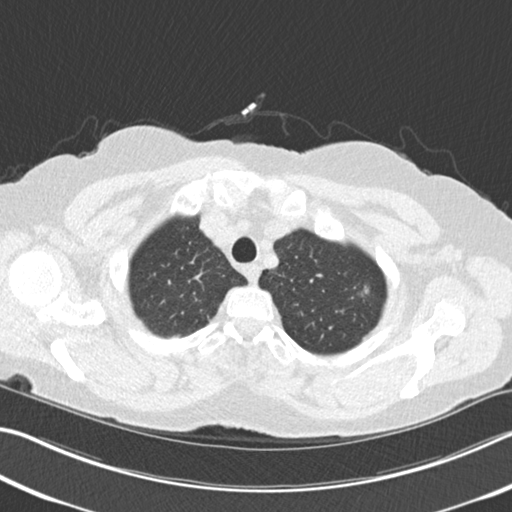
Chest CT (low-dose screening protocol), one axial image, second screening round (one year after baseline), lung window (W 1500 / L -600 HU), standard (soft-tissue) reconstruction kernel (B30f), slice 29 of 225 in the series, 512 × 512 image matrix. Female participant, aged 64 years at enrolment.
- Expert-annotated lung lesion, bounding box (x1, y1, x2, y2) in pixels: (343, 274, 377, 307).
- Screening reader's record for this exam (one nodule recorded; not confirmed to be the boxed lesion): non-calcified nodule or mass ≥4 mm, left upper lobe, 13 × 10 mm, spiculated (stellate) margins, soft tissue attenuation, pre-existing on the prior screen: yes; interval growth: yes.
- Official screen result: positive, other.
- Later outcome: lung cancer diagnosed 106 days after this screen — signet ring cell carcinoma, right upper lobe, poorly differentiated (G3), stage IA (AJCC 6th edition), 15 mm at pathology.